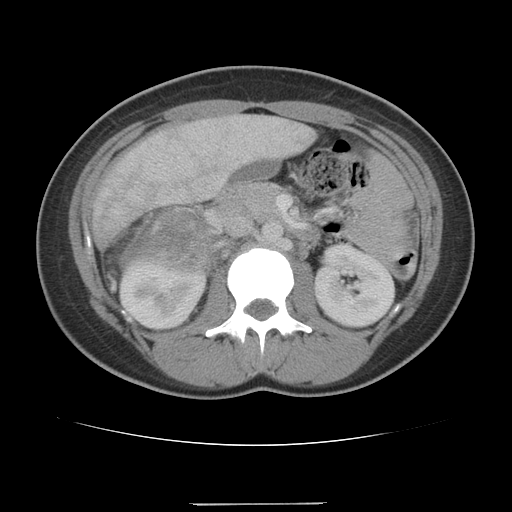
Contrast-enhanced abdominal CT, one axial slice. Position 61 of 100 along the scan axis. Reconstruction kernel STANDARD. Intravenous contrast given. Soft-tissue window (W 400 / L 40 HU). 512 × 512 image matrix, field of view 360 × 360 mm. Patient: female, 21 years. Case-level facts recorded for this patient, not image findings: diagnosis: adrenocortical carcinoma; tumour side: right adrenal; tumour size at pathology: 15.5 cm; Ki-67 index: 26 %.
Structures marked on this image (semi-automatic segmentation, software-assisted and operator-edited):
- mass: bounding box (x1, y1, x2, y2) in pixels: (122, 210, 211, 270)